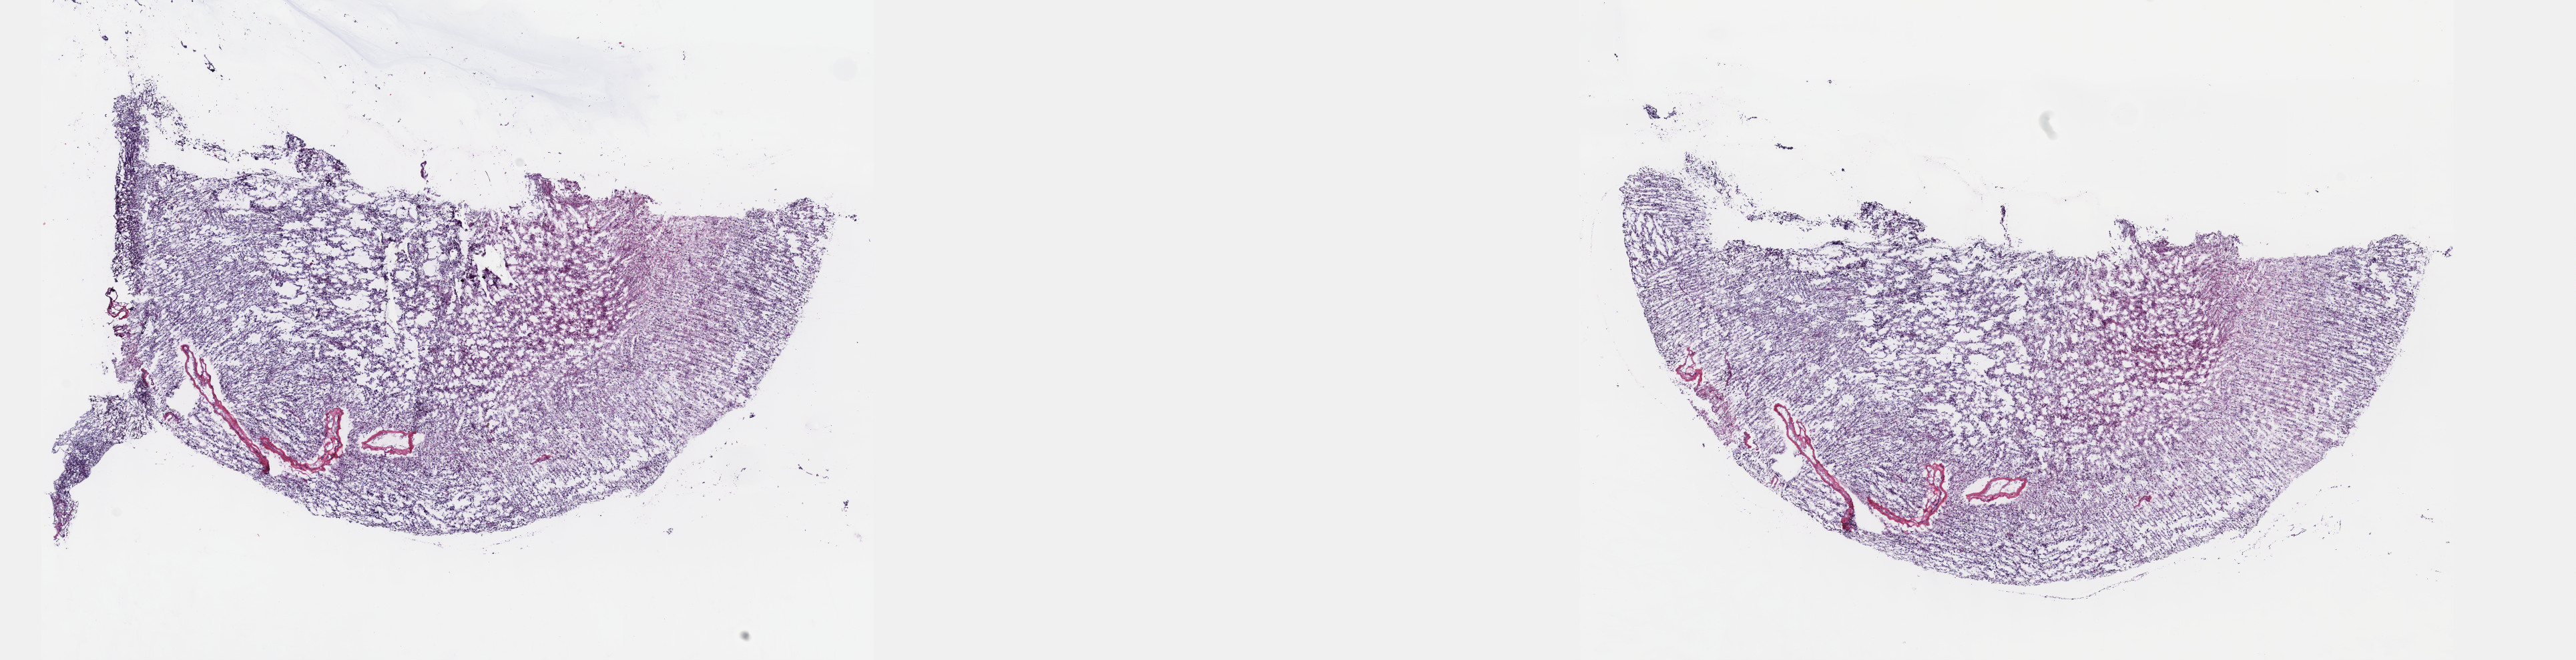
Hematoxylin and eosin (H&E) stained whole-slide image, low-resolution overview of the scanned area, about 31.2 x 8.0 mm, frozen section, brain, primary tumour sample. Female, age 36 years at initial diagnosis. Histologic grade: G3 (poorly differentiated). Slide review estimates, as recorded: tumour cells 60%, tumour nuclei 90%, normal cells 10%, stromal cells 30%, necrosis 0%. Infiltration values recorded for this section: lymphocyte infiltration 0%, monocyte infiltration 0%, neutrophil infiltration 0%.
Pathologic diagnosis: Astrocytoma, anaplastic (cerebrum).